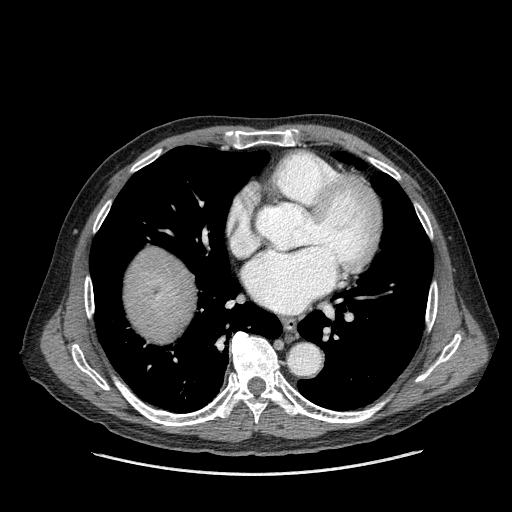
Contrast-enhanced abdominal CT (liver protocol), one axial slice. Position 162 of 180 along the scan axis. 120 kVp. One of 2 acquisitions stored at this slice position. Soft-tissue window (W 400 / L 40 HU). 2.5 mm slice thickness. 512 × 512 image matrix. From the clinical record (not read from this slice): diagnosis: hepatocellular carcinoma (patient treated with transarterial chemoembolisation; whether this scan precedes or follows treatment is not stated here); TNM stage (as recorded): Stage-II; Child-Pugh class: A; tumour differentiation: well differentiated; tumour nodularity: multinodular.
Annotated regions visible in this slice (semi-automatically segmented with operator editing):
- liver parenchyma outside the tumour (the mass and vessels are separate outlines, so this box may not span the whole liver): box from (x=124, y=246) to (x=196, y=342) px
- mass: (x=140, y=272)–(x=166, y=303)